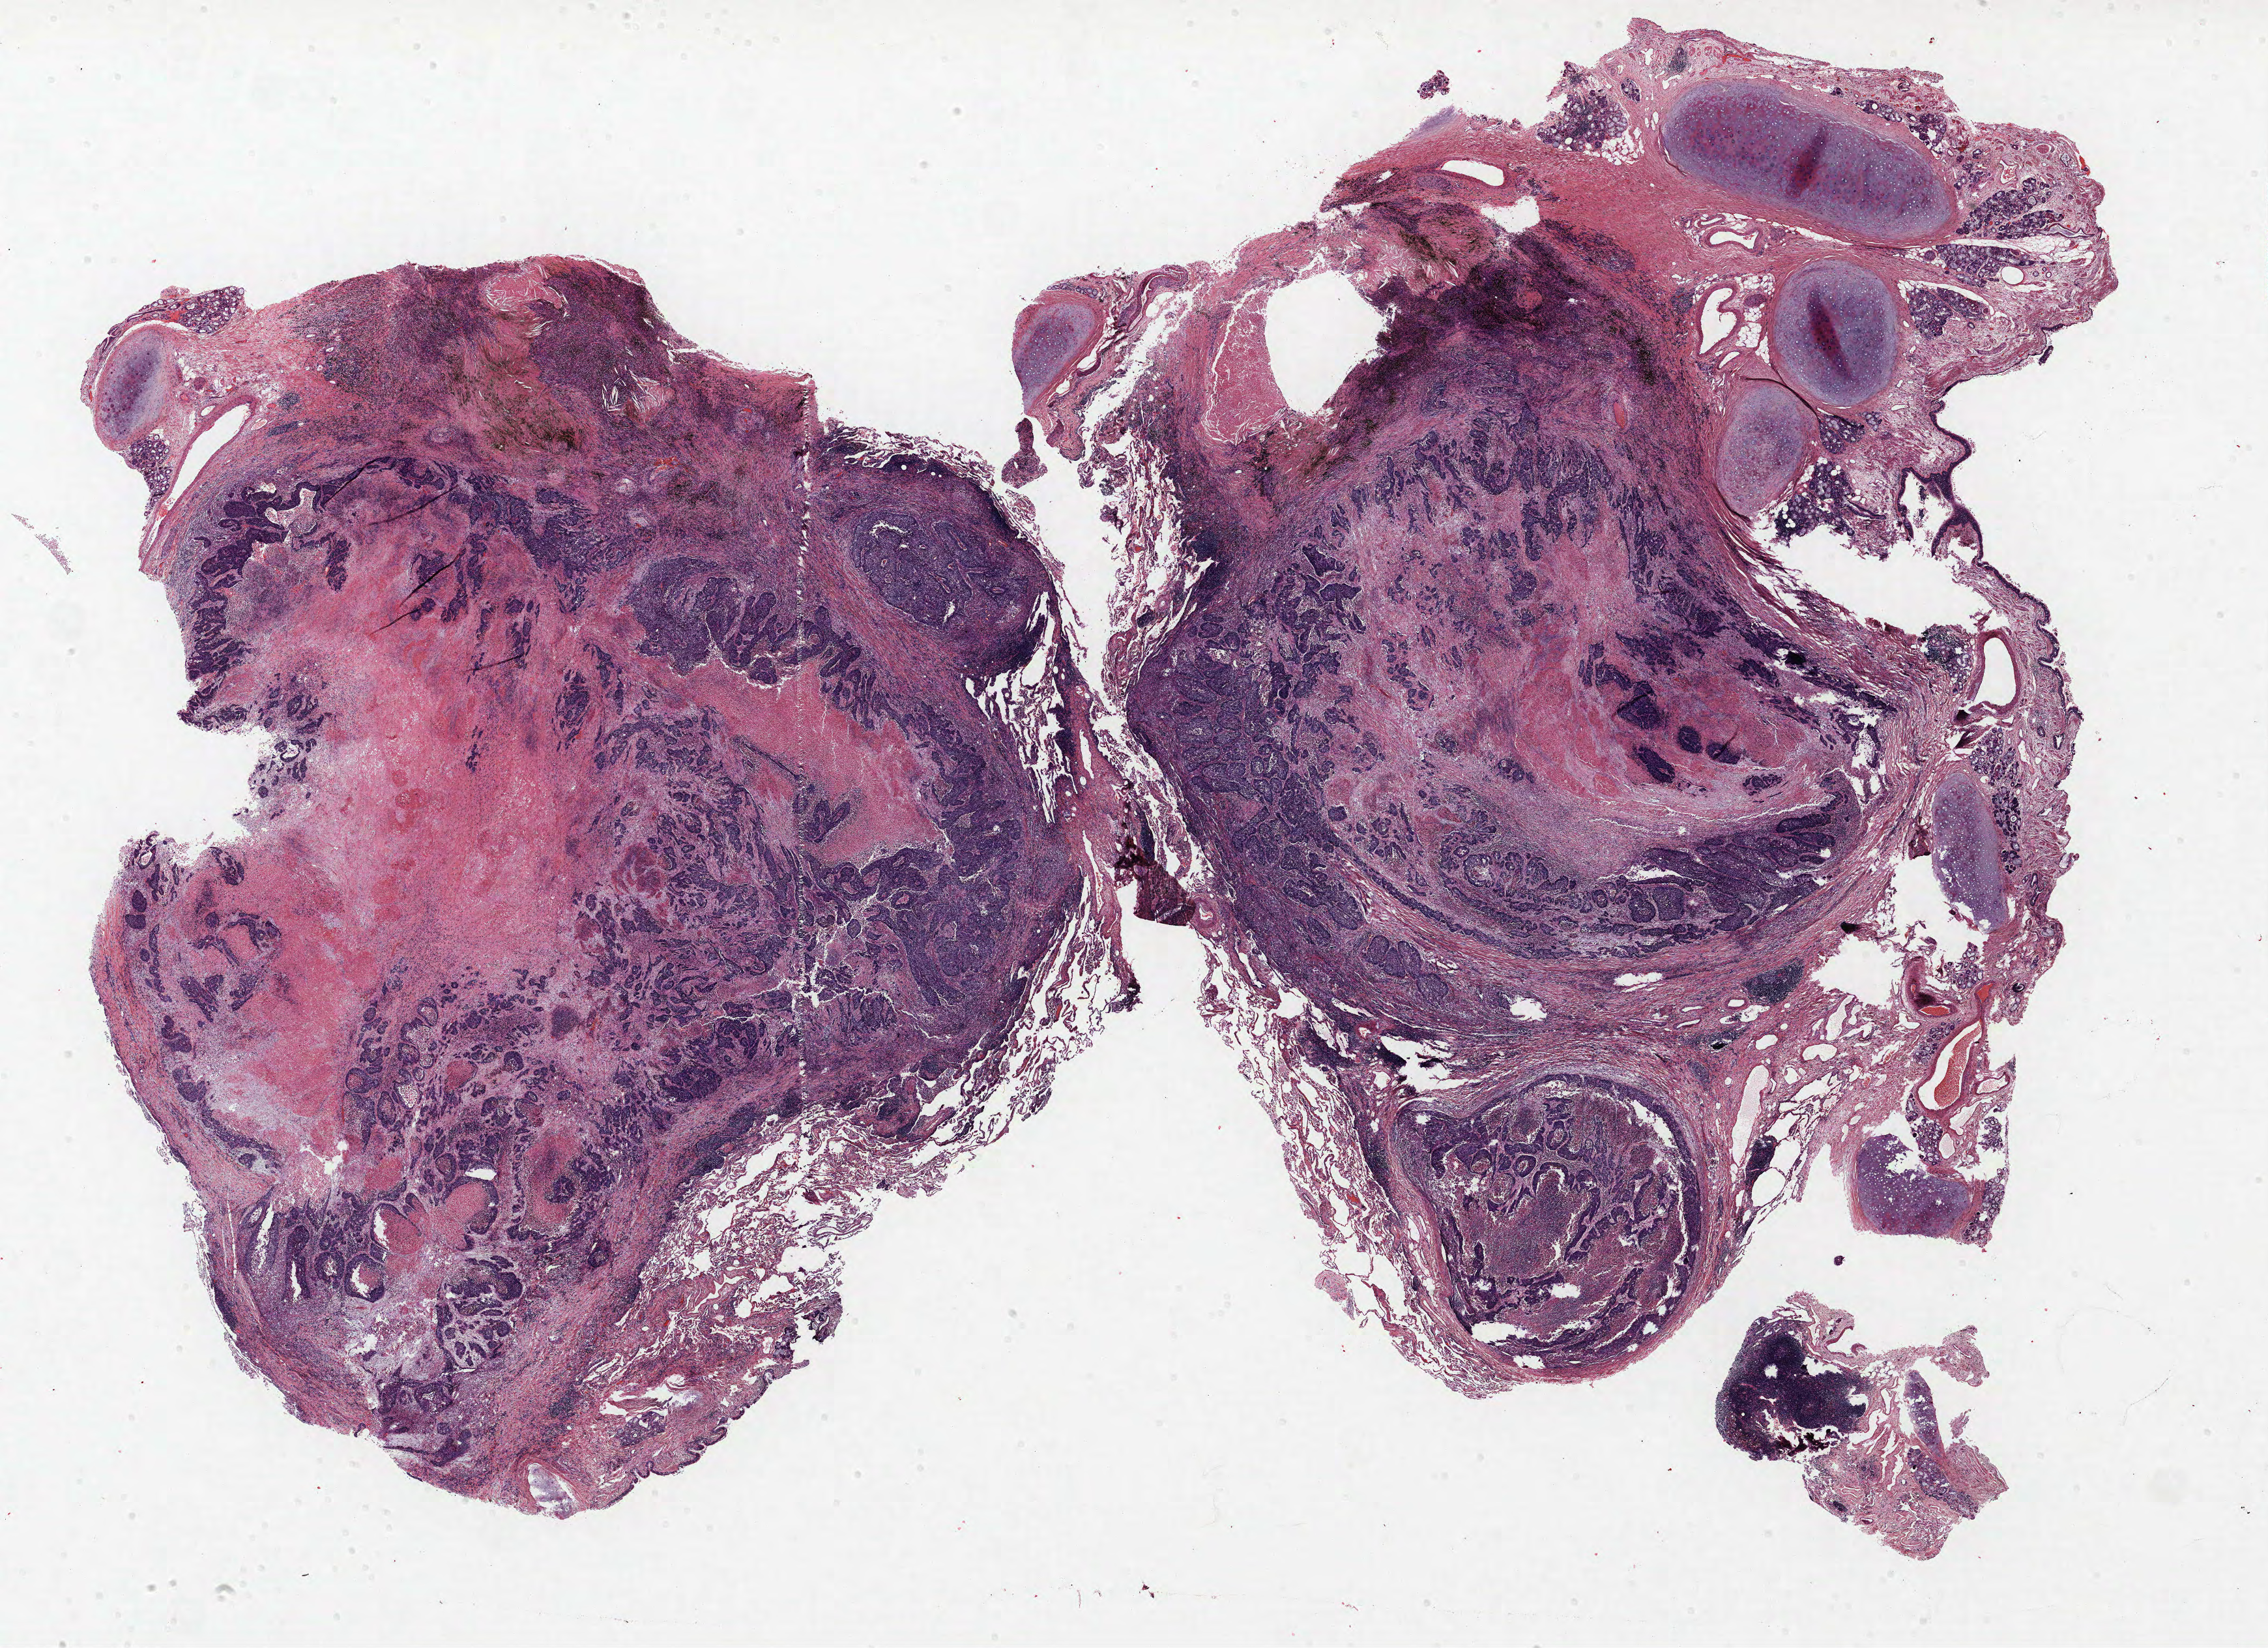
Hematoxylin and eosin (H&E) stained whole-slide image — whole scanned area (about 27.8 x 20.2 mm) shown as a low-resolution overview; FFPE section; lung tissue. Male, age 68 at enrolment.
Participant's lung-cancer diagnosis: Squamous cell carcinoma, NOS.